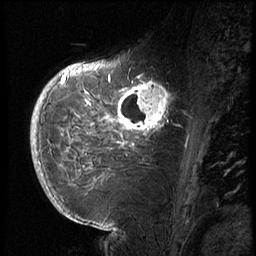
Breast MRI (dynamic contrast-enhanced), one sagittal slice. Slice 23 of 72 in the series (ordered by position). 3 images stored at this slice position (order not interpretable as contrast timing). 1.5 T. TE 4.2 ms, TR 8.9 ms. 2.5 mm slice thickness. 256 × 256 image matrix, field of view 200 × 200 mm. Female patient, age 56 years. Case-level facts recorded for this patient, not image findings: setting: breast cancer imaged before/during neoadjuvant chemotherapy.
Annotated regions visible in this slice (semi-automatic segmentation, software-assisted and operator-edited):
- analysis volume of interest (the breast-tissue region the enhancement analysis was run in; not a lesion): bounding box <114,76,177,138> (left, top, right, bottom; pixels)
- tumour enhancement mask (voxels above the 140 % enhancement threshold inside the analysis volume of interest): <117,77,172,132>